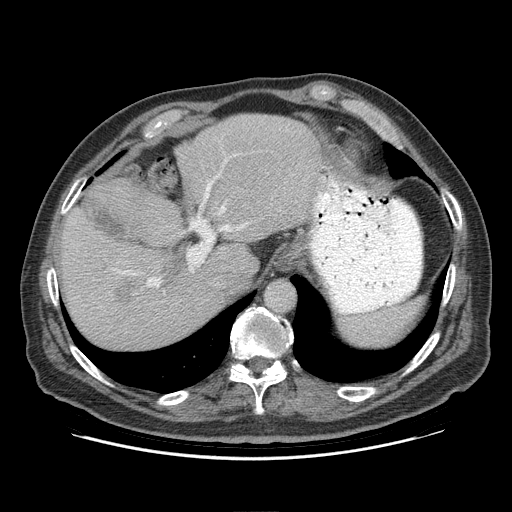
Contrast-enhanced abdominal CT (liver protocol), one axial slice. Position 70 of 95 along the scan axis. Reconstruction kernel STANDARD. Soft-tissue window (W 400 / L 40 HU). 2.5 mm slice thickness. 512 × 512 image matrix, field of view 400 × 400 mm. From the clinical record (not read from this slice): diagnosis: hepatocellular carcinoma (patient treated with transarterial chemoembolisation; whether this scan precedes or follows treatment is not stated here); TNM stage (as recorded): Stage-IVB; Child-Pugh class: A.
Structures marked on this image (semi-automatically segmented with operator editing):
- abdominal aorta: bounding box [x1, y1, x2, y2] px = [266, 281, 293, 312]
- liver parenchyma outside the tumour (the mass and vessels are separate outlines, so this box may not span the whole liver): [60, 114, 326, 348]
- mass: [107, 275, 145, 308]
- liver vessels: [118, 176, 246, 287]